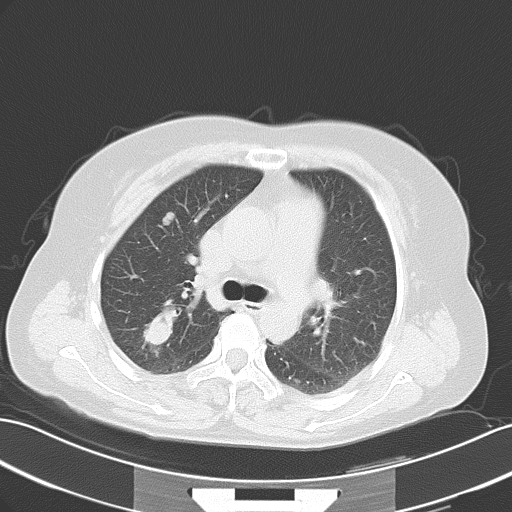
Chest CT, one axial slice. Position 33 of 49 along the scan axis. Lung window (W 1500 / L -600 HU). 5 mm slice thickness. 512 × 512 image matrix. Patient: female, 52 years. From the clinical record (not read from this slice): clinical TNM (as recorded): T1c N3 M1a.
Structures marked on this image (rectangle marked by the reading radiologist):
- lung tumour (recorded histology: adenocarcinoma): box from (x=133, y=295) to (x=184, y=353) px